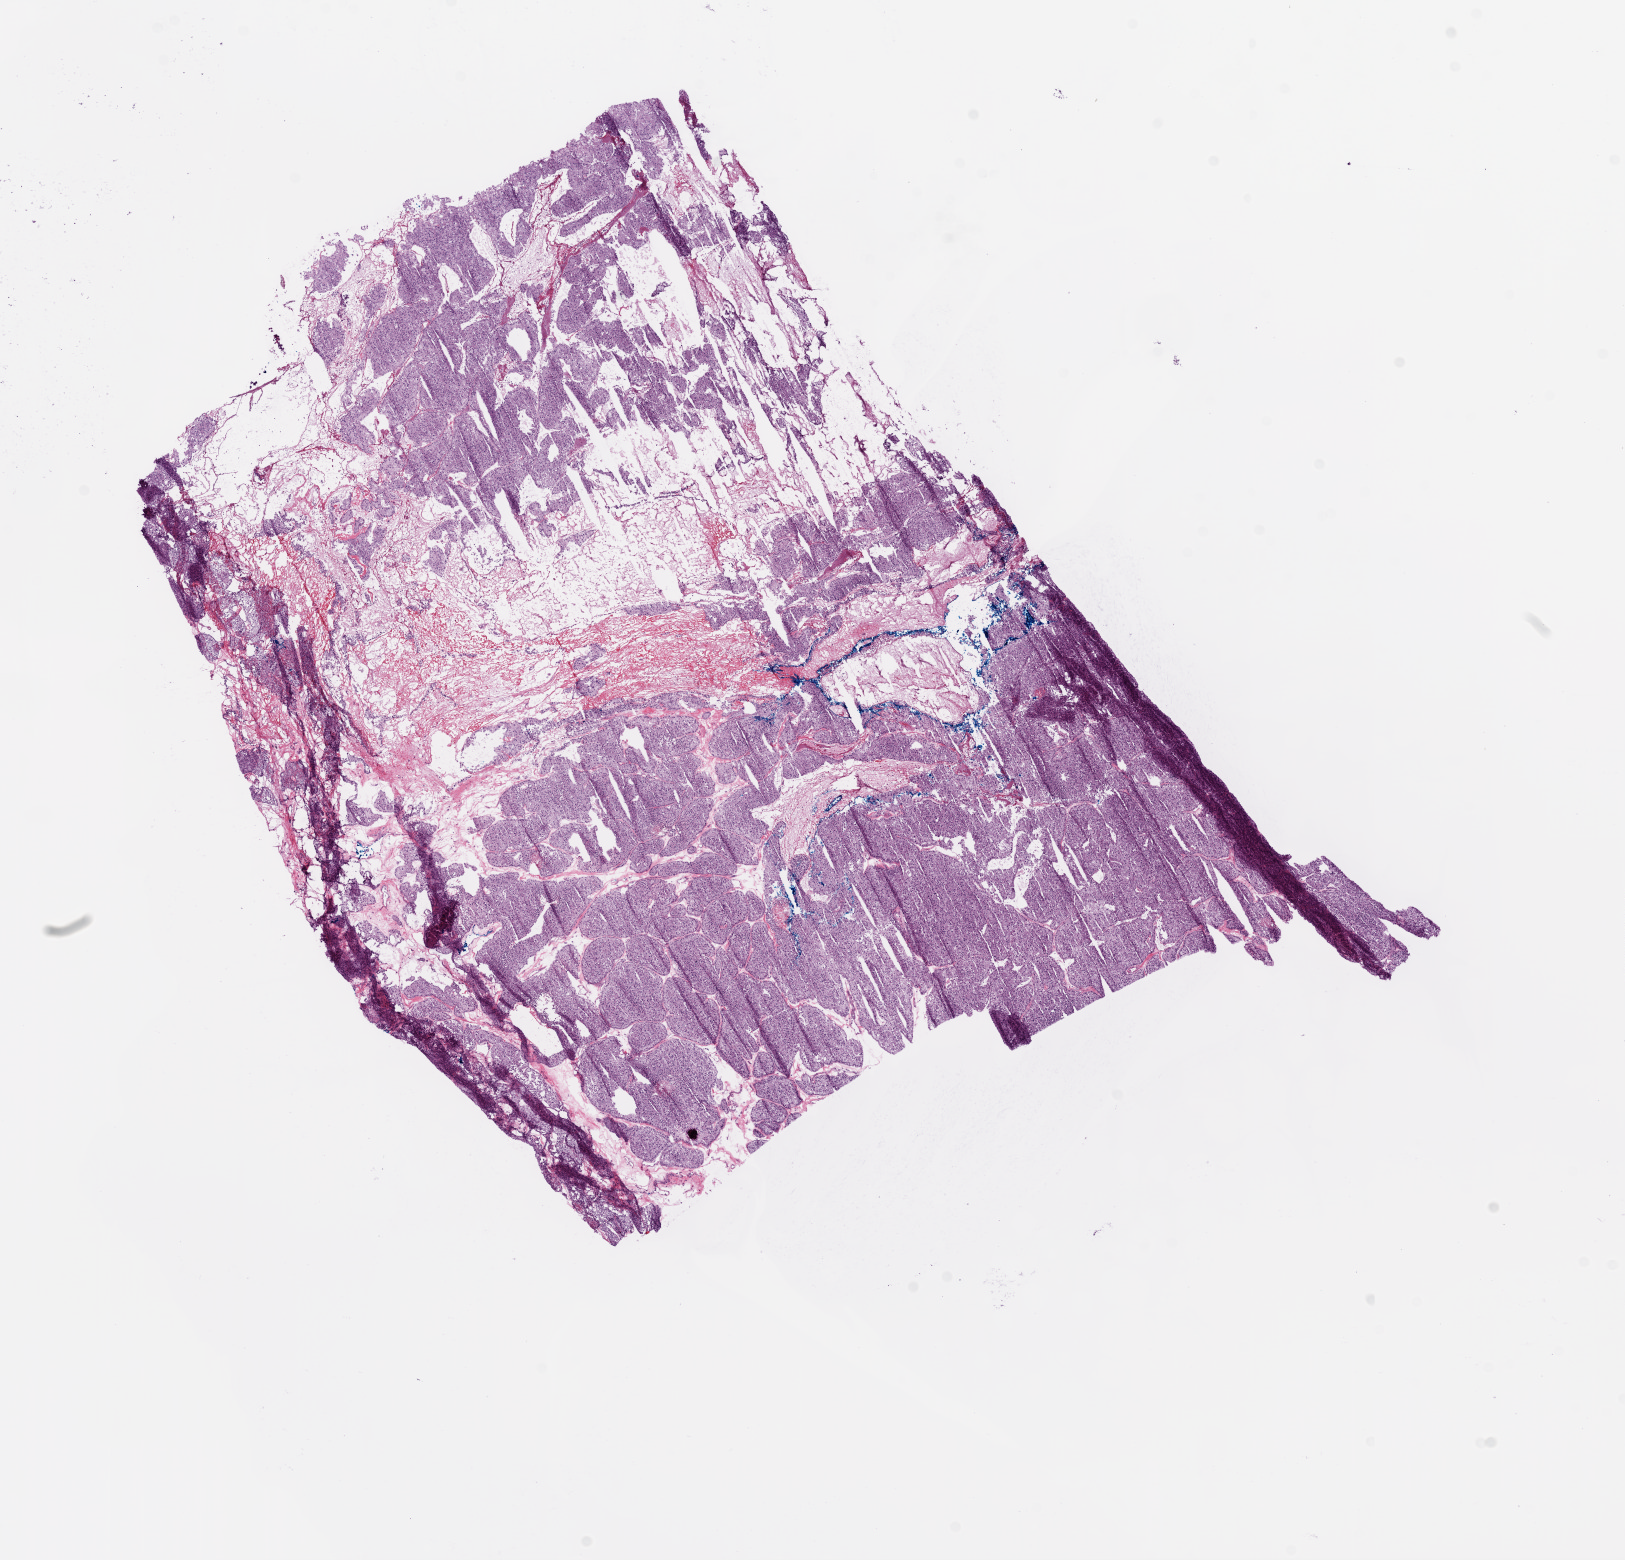
H&E-stained whole-slide image — shown as a low-resolution overview of the whole scanned area (about 13.0 x 12.5 mm, from a 20x scan). Frozen section from the bottom of the tissue portion. Primary tumour sample from the kidney. Patient: male, age at initial diagnosis 79 years. Histologic grade: G2 (moderately differentiated). Pathologist review of this section (percent, as recorded): tumour cells 75%, tumour nuclei 90%, normal cells 0%, stromal cells 5%, necrosis 20%.
* diagnosis: Clear cell adenocarcinoma, NOS
* AJCC pathologic stage: I
* TNM: T1b N0 M0